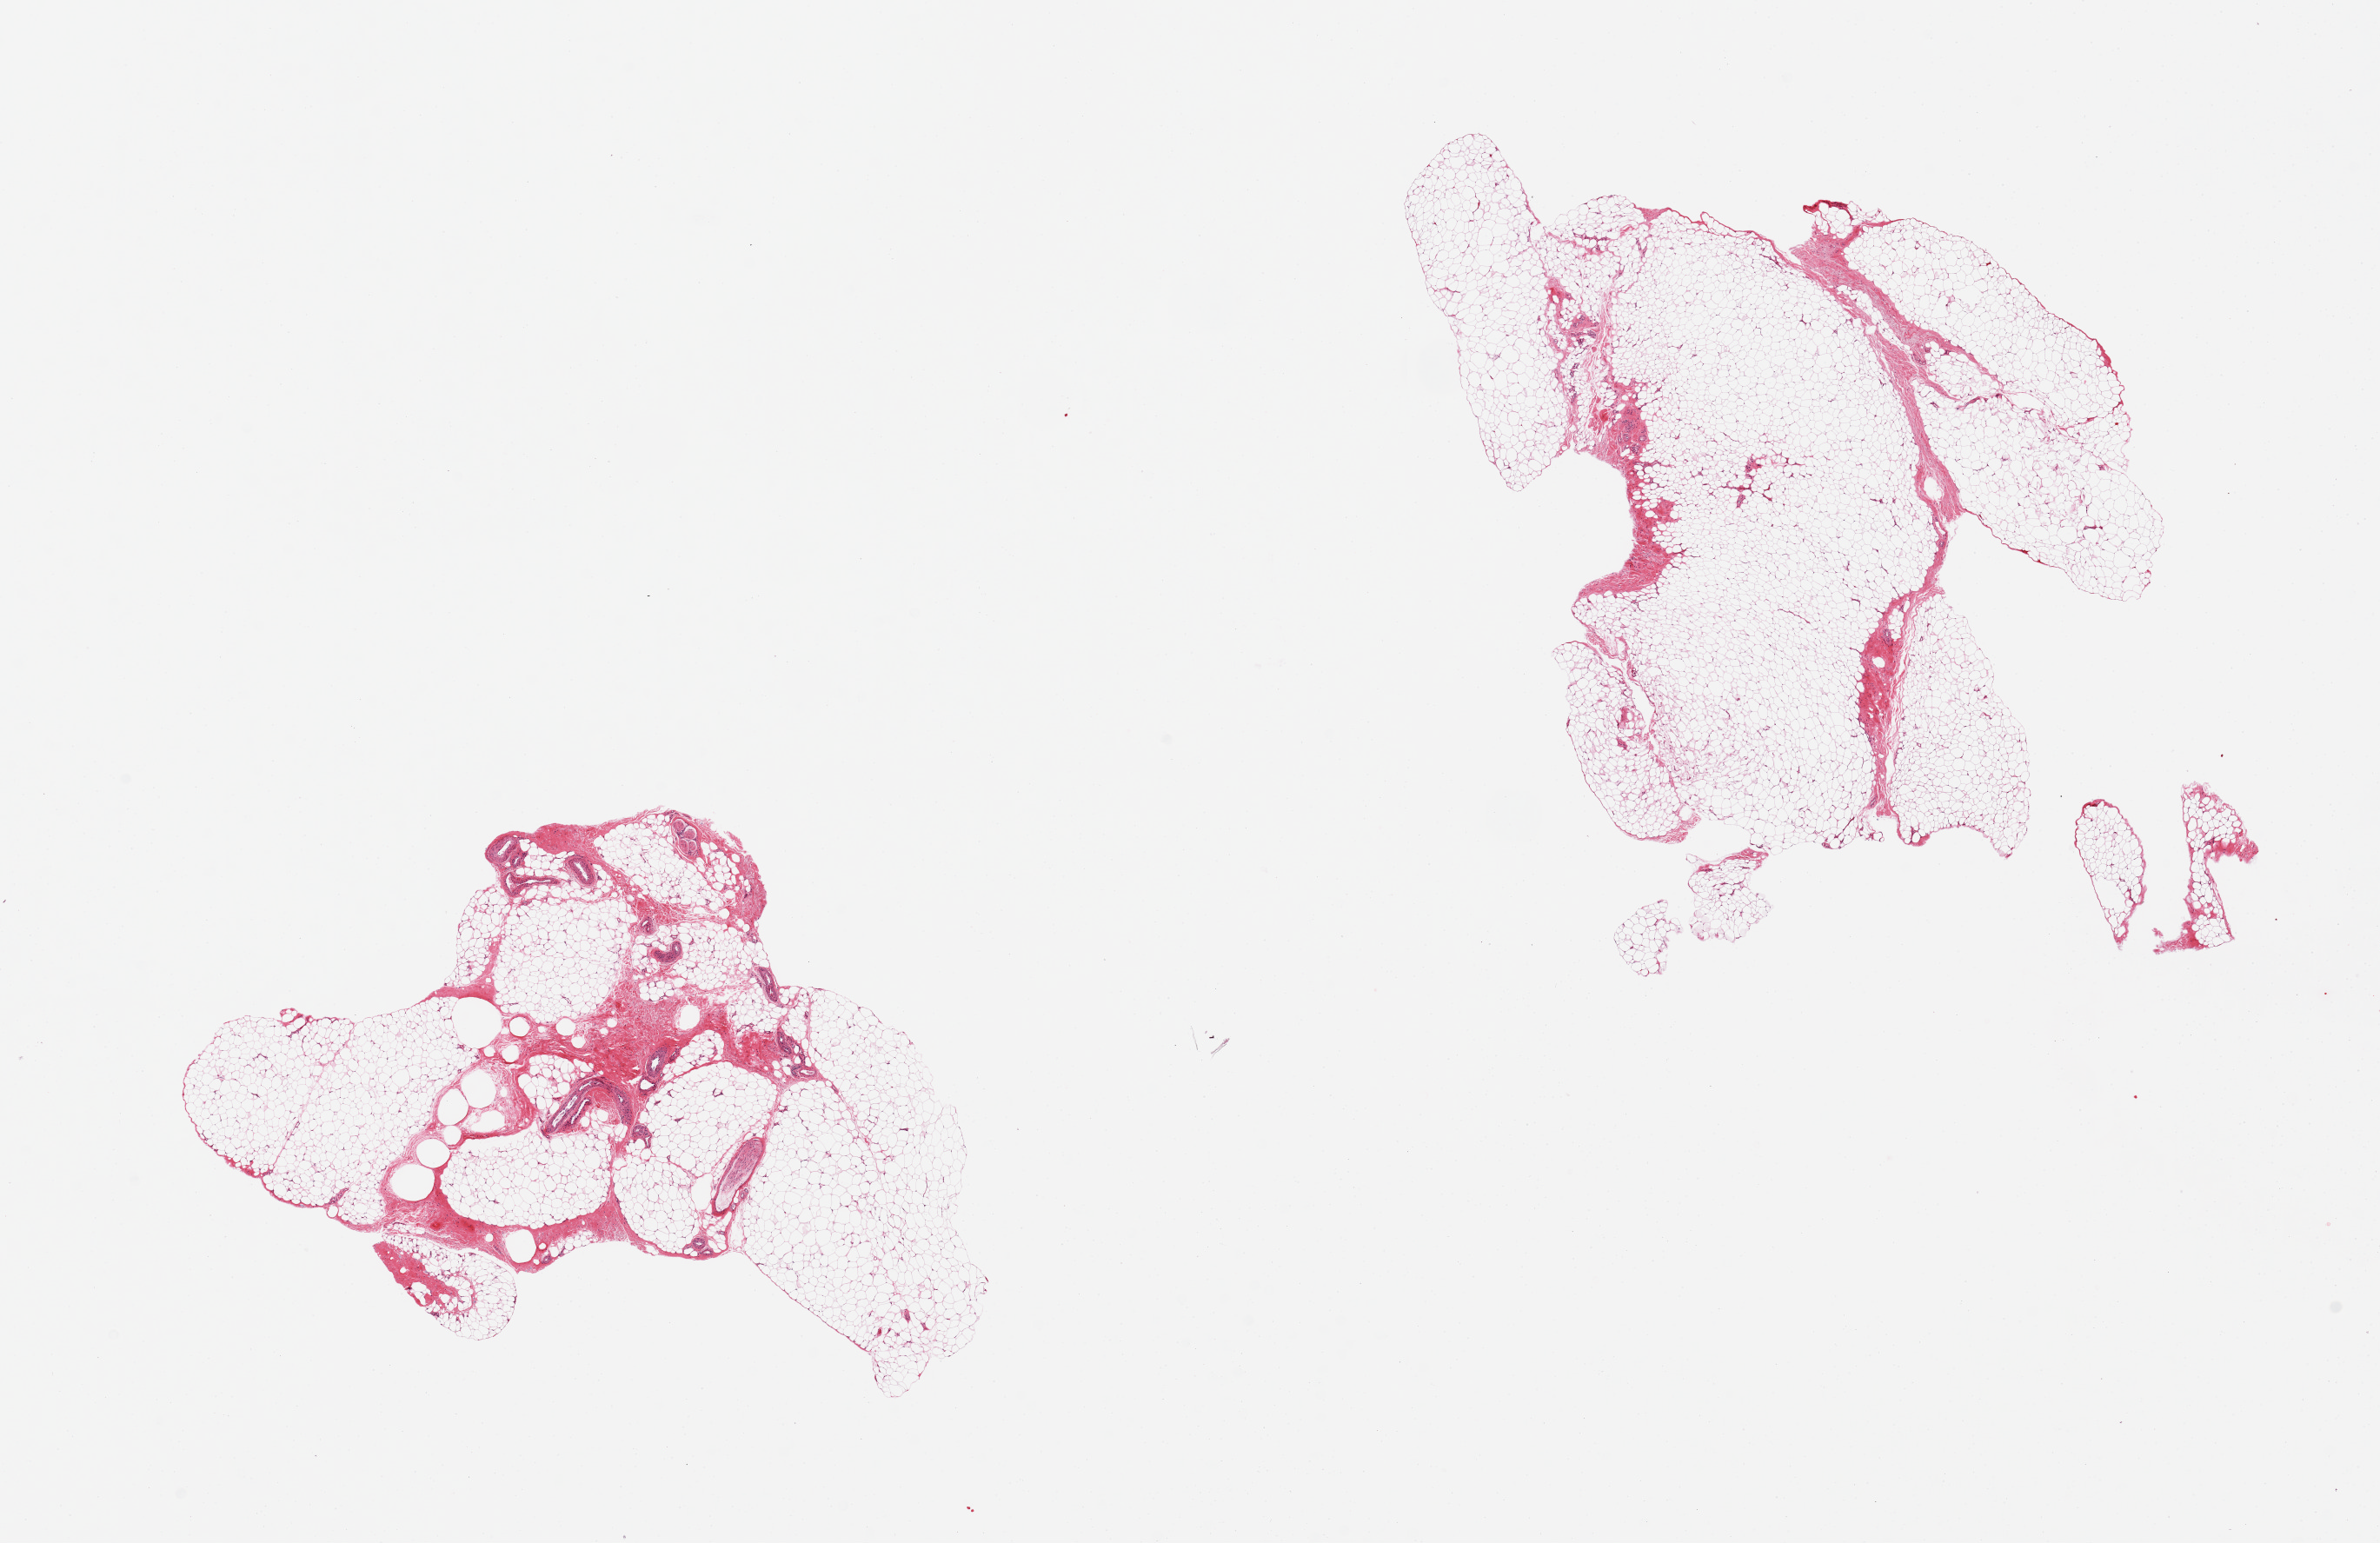
Whole-slide image, H&E stain, brightfield, shown as a low-resolution overview of the whole scanned area (about 21.7 x 14.0 mm), PAXgene-fixed, paraffin-embedded tissue, sampled site (target tissue): adipose tissue, donor tissue sample. Donor sex: male.
• pathologist's review note for this sample: 2pieces, ~30% fibrous connective/fascia; peripheral nerves/vessels entrapped/